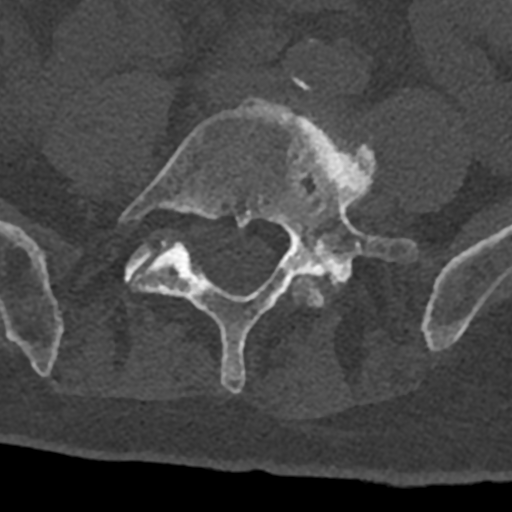
CT including the spine, one axial slice. Position 205 of 797 along the scan axis. Reconstruction kernel Br40s/3. 120 kVp. Bone window (W 1800 / L 400 HU). 512 × 512 image matrix, field of view 160 × 160 mm. Male patient, age 74 years. From the clinical record (not read from this slice): primary cancer: renal; vertebrae with lytic lesions (as recorded): T10, L1, L2, L3, L4, L5.
Annotated regions visible in this slice (semi-automatic segmentation, software-assisted and operator-edited):
- L4 vertebra: box from (x=287, y=135) to (x=372, y=308) px
- L5 vertebra: (x=119, y=98)–(x=418, y=393)